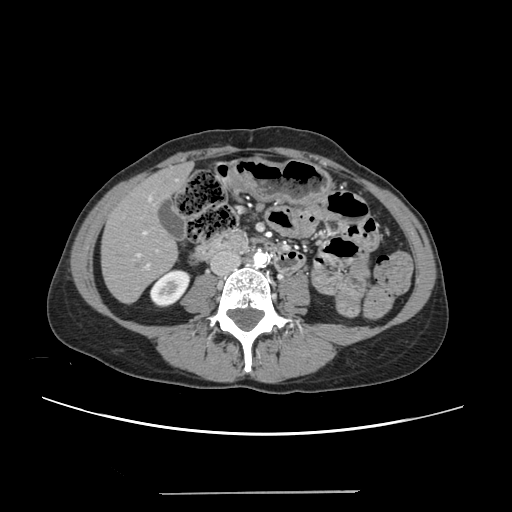
Contrast-enhanced abdominal CT, one axial slice; position 68 of 240 along the scan axis; intravenous contrast given; soft-tissue window (W 400 / L 40 HU); 1.25 mm slice thickness; 512 × 512 image matrix. Female patient, age 60 years. From the clinical record (not read from this slice): diagnosis: colorectal cancer liver metastases, imaged before liver resection; multiple liver metastases: no; largest metastasis: 1.5 cm; chemotherapy before resection: yes.
Structures marked on this image (expert manual segmentation):
- liver: bounding box (x1, y1, x2, y2) in pixels: (103, 166, 188, 301)
- planned liver remnant (the part of the liver to remain after resection): (103, 171, 177, 302)
- portal vein (with intrahepatic branches): (137, 197, 158, 268)